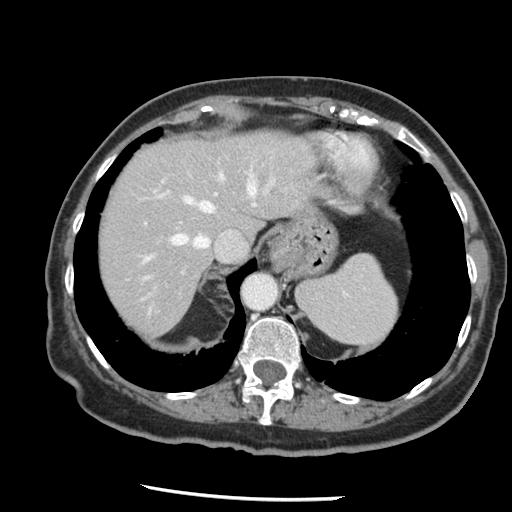
Contrast-enhanced abdominal CT, one axial slice. Slice 108 of 148 in the series (ordered by position). Intravenous contrast given. Soft-tissue window (W 400 / L 40 HU). 2.5 mm slice thickness. 512 × 512 image matrix. Female patient, age 85 years. From the clinical record (not read from this slice): diagnosis: colorectal cancer liver metastases, imaged before liver resection; multiple liver metastases: no; largest metastasis: 0.9 cm; chemotherapy before resection: yes.
Annotated regions visible in this slice (outlined manually by an expert reader):
- hepatic veins: box from (x=141, y=161) to (x=275, y=261) px
- liver: (x=98, y=130)–(x=316, y=337)
- planned liver remnant (the part of the liver to remain after resection): (x=98, y=130)–(x=316, y=337)
- portal vein (with intrahepatic branches): (x=142, y=192)–(x=218, y=281)